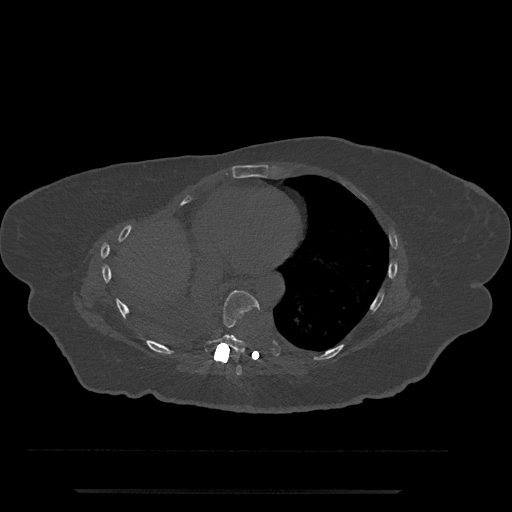
CT including the spine, one axial slice. Position 391 of 797 along the scan axis. 120 kVp. Bone window (W 1800 / L 400 HU). 0.5 mm slice thickness. 512 × 512 image matrix. Female patient, age 51 years. Case-level facts recorded for this patient, not image findings: primary cancer: neuro.
Annotated regions visible in this slice (semi-automatically segmented with operator editing):
- T7 vertebra: bounding box <234,365,242,375> (left, top, right, bottom; pixels)
- T8 vertebra: <203,290,260,353>